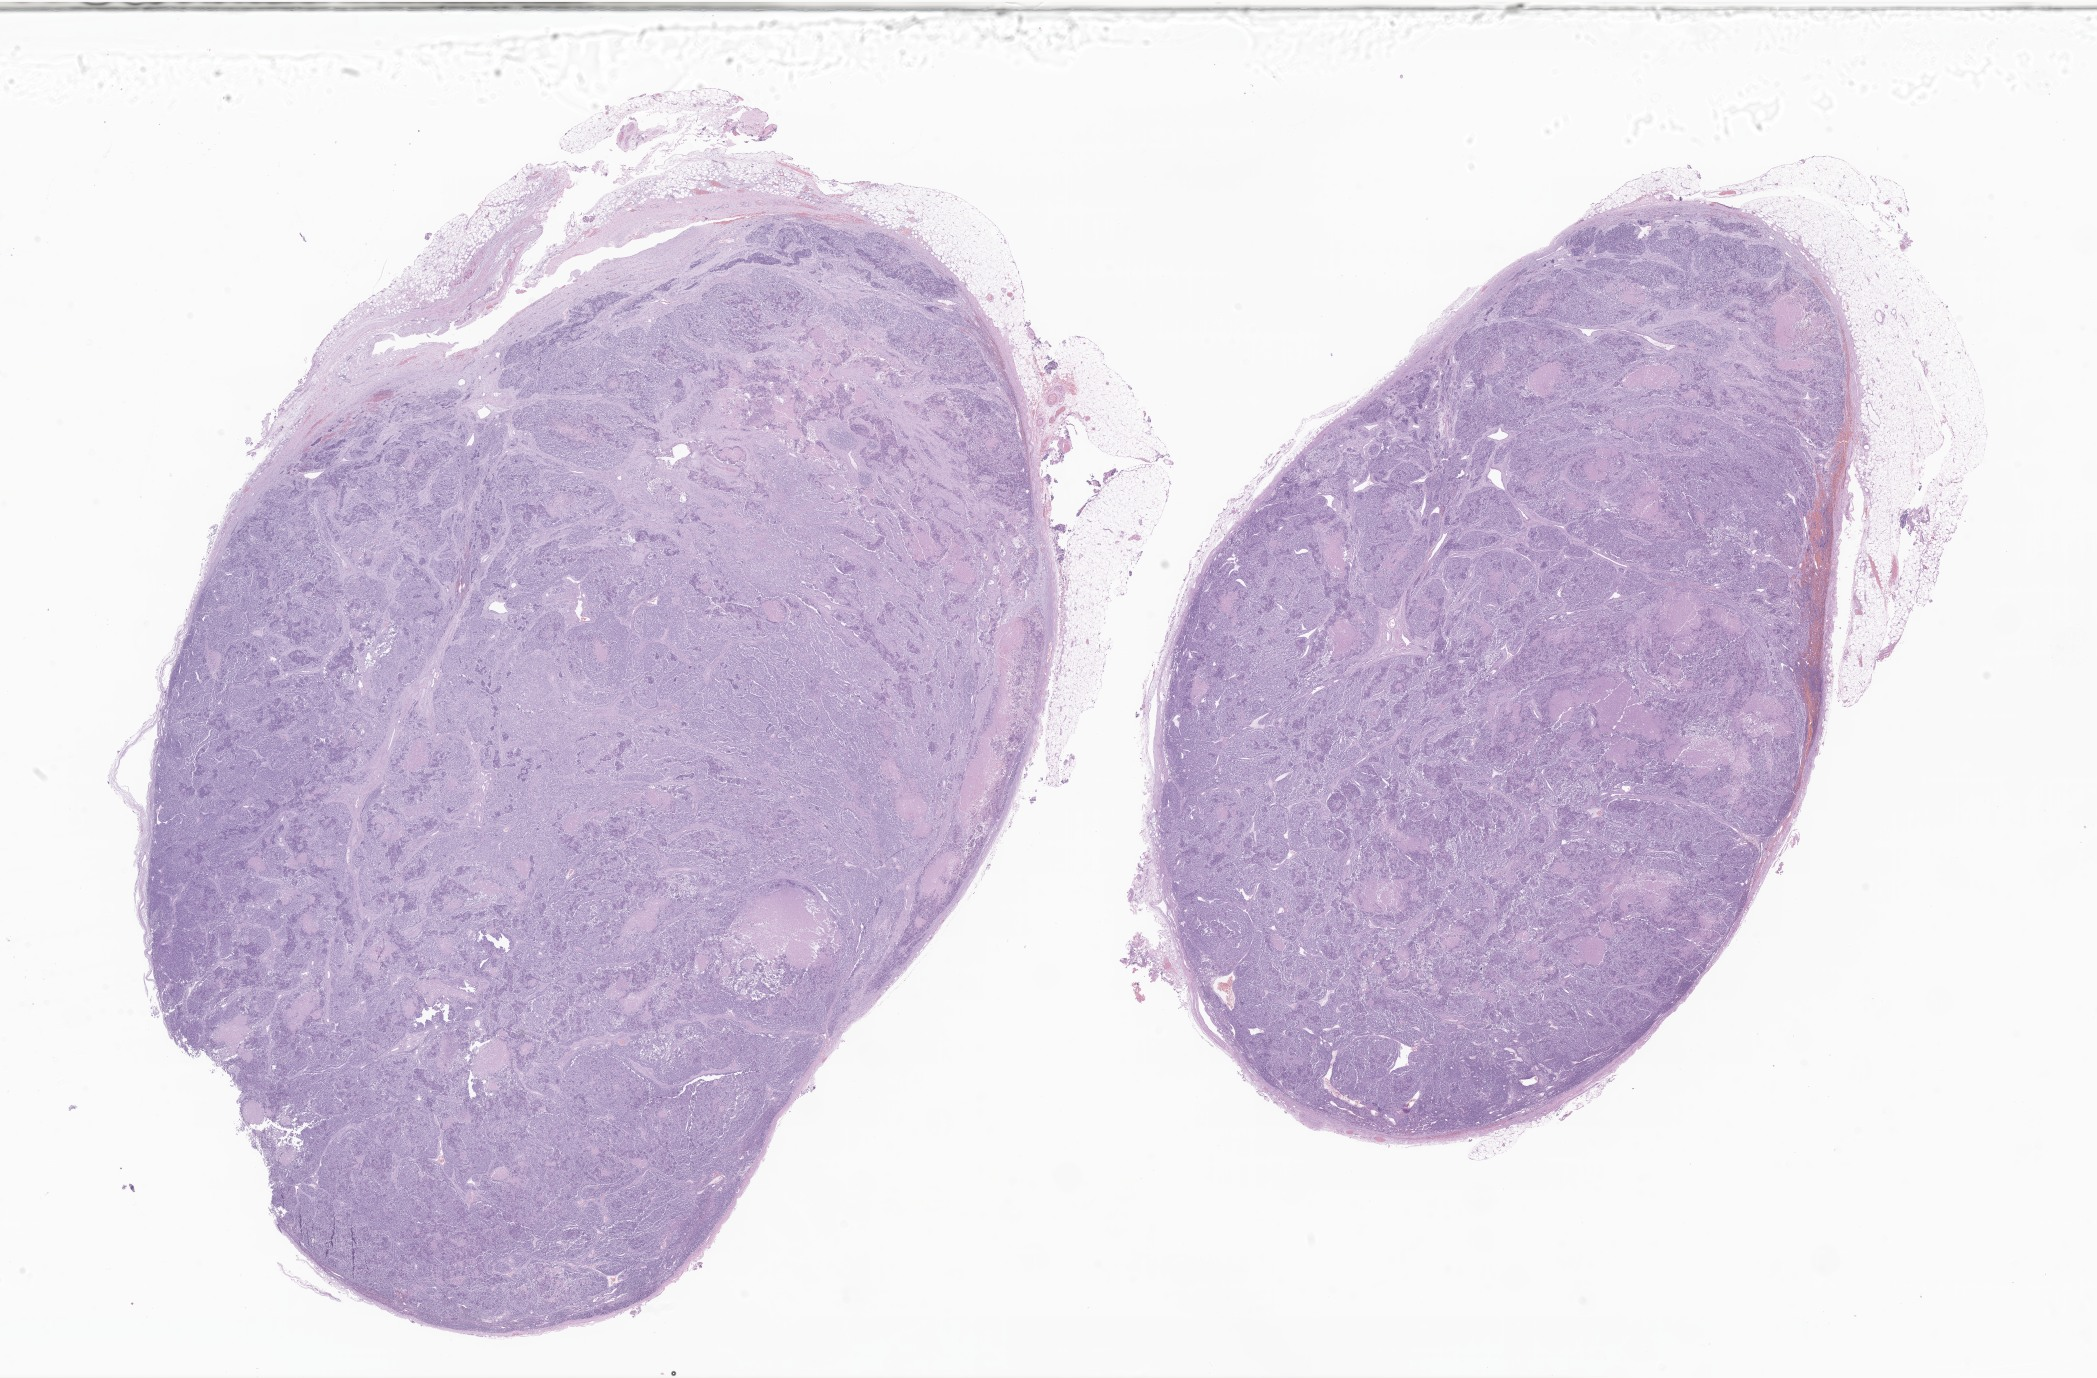
H&E whole-slide image of tumor tissue from the soft tissue of pelvis — a low-resolution overview of the entire scanned area, about 35.4 x 23.2 mm. FFPE section. Patient: female, age 145 months (12 years 1 month).
Tissue or organ of origin (case record): connective, subcutaneous and other soft tissues of pelvis. Diagnosis (ICD-O-3 morphology term): Alveolar rhabdomyosarcoma.